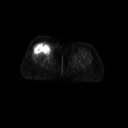
FDG PET of an extremity soft-tissue mass (from a PET/CT study), one axial slice. Slice 28 of 267 in the series (ordered by position). 128 × 128 image matrix, field of view 700 × 700 mm. Patient: female, 56 years. From the clinical record (not read from this slice): histological type: malignant solitary fibrous tumor; grade: intermediate; site of the primary tumour: right thigh.
Annotated regions visible in this slice (expert contour drawn on MRI and transferred to this co-registered scan by the dataset authors):
- gross tumour volume including surrounding oedema: bounding box <36,41,55,57> (left, top, right, bottom; pixels)
- gross tumour volume (mass): <36,42,54,55>